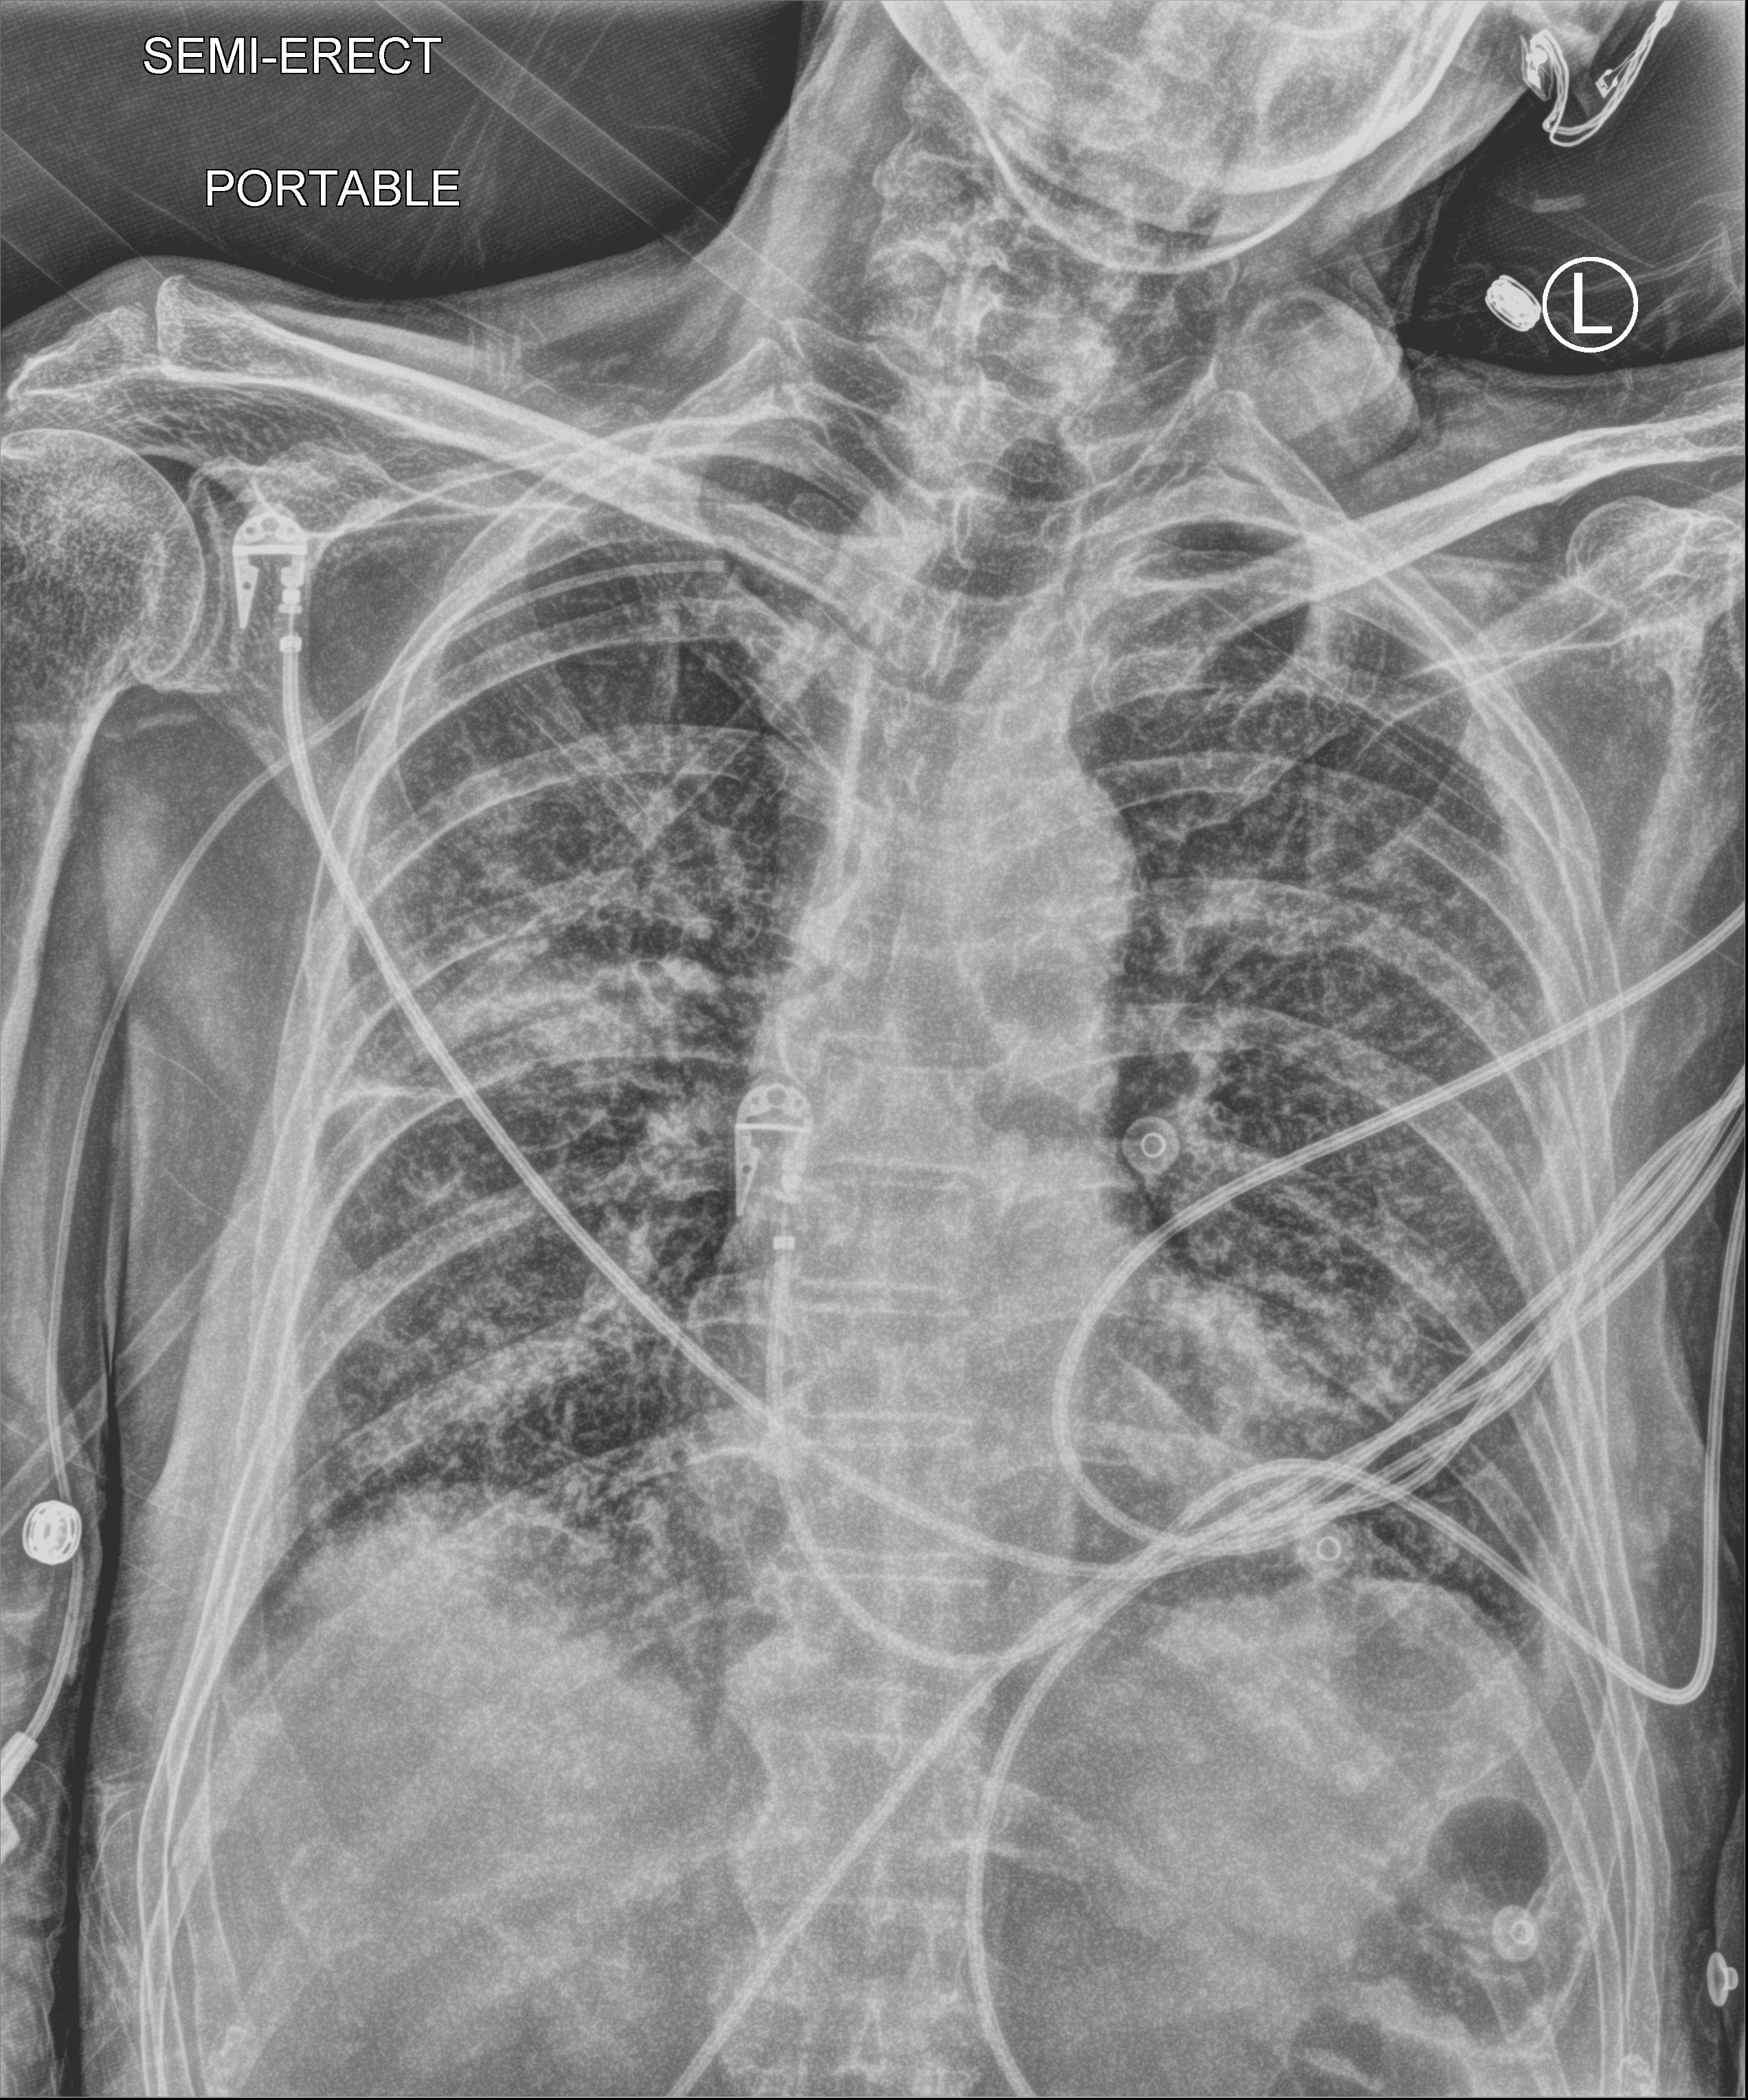
Portable chest radiograph; anteroposterior (AP) projection. Male patient hospitalised with COVID-19, age 60–74 years.
Hospital-stay facts (about this admission, not read from this image; timing relative to this image not recorded):
- admitted to intensive care during this hospital stay: yes